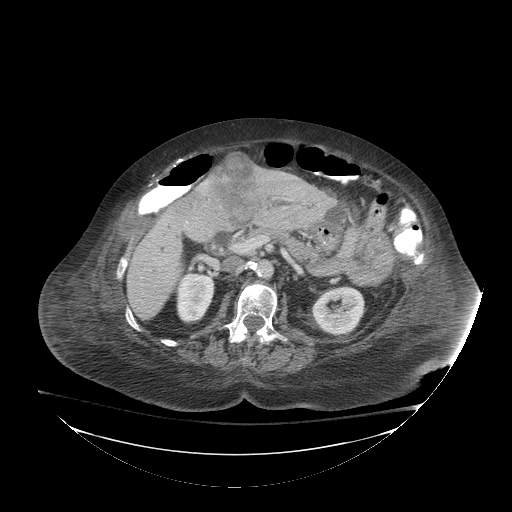
Contrast-enhanced abdominal CT (liver protocol), one axial slice; position 34 of 81 along the scan axis; reconstruction kernel STANDARD; soft-tissue window (W 400 / L 40 HU); 512 × 512 image matrix. Case-level facts recorded for this patient, not image findings: diagnosis: hepatocellular carcinoma (patient treated with transarterial chemoembolisation; whether this scan precedes or follows treatment is not stated here); TNM stage (as recorded): Stage-I; Child-Pugh class: B; tumour differentiation: well-moderately differentiated; tumour nodularity: uninodular.
Outlined on this slice (semi-automatic segmentation, software-assisted and operator-edited):
- liver parenchyma outside the tumour (the mass and vessels are separate outlines, so this box may not span the whole liver): bounding box (x1, y1, x2, y2) in pixels: (126, 174, 312, 320)
- mass: (209, 152, 260, 222)